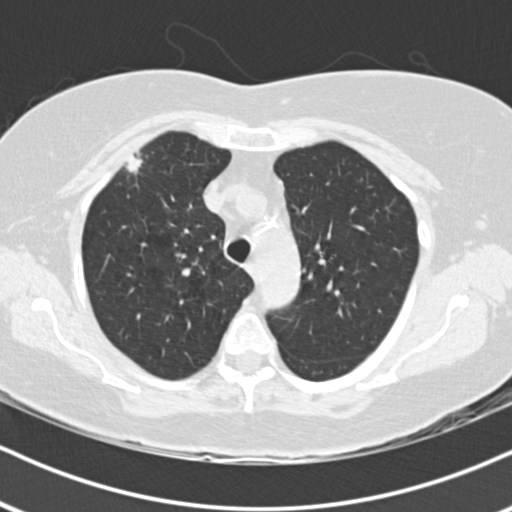
Low-dose screening chest CT, one axial slice; slice 137 of 178 in the series (ordered by position); 120 kVp; lung window (W 1500 / L -600 HU); 512 × 512 image matrix, field of view 320 × 320 mm.
Structures marked on this image (expert manual segmentation):
- lesion 1 (tumor, upper lobe of right lung): bounding box (x1, y1, x2, y2) in pixels: (123, 154, 143, 175)